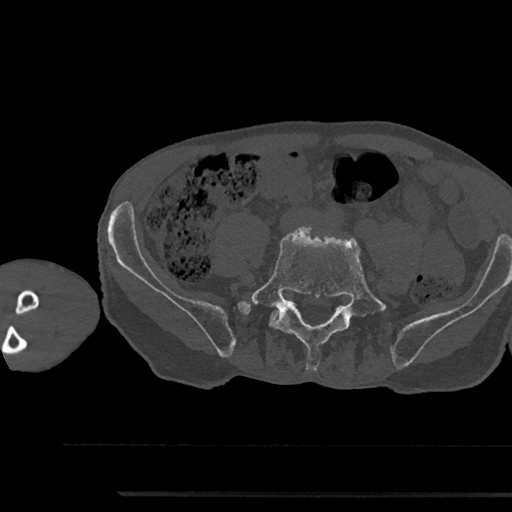
CT including the spine, one axial slice. Slice 348 of 797 in the series (ordered by position). Reconstruction kernel Br40s/3. Bone window (W 1800 / L 400 HU). 0.5 mm slice thickness. 512 × 512 image matrix, field of view 367 × 367 mm. Patient: male, 79 years. Case-level facts recorded for this patient, not image findings: primary cancer: prostate.
Annotated regions visible in this slice (semi-automatic segmentation, software-assisted and operator-edited):
- L5 vertebra: box from (x=244, y=227) to (x=388, y=370) px